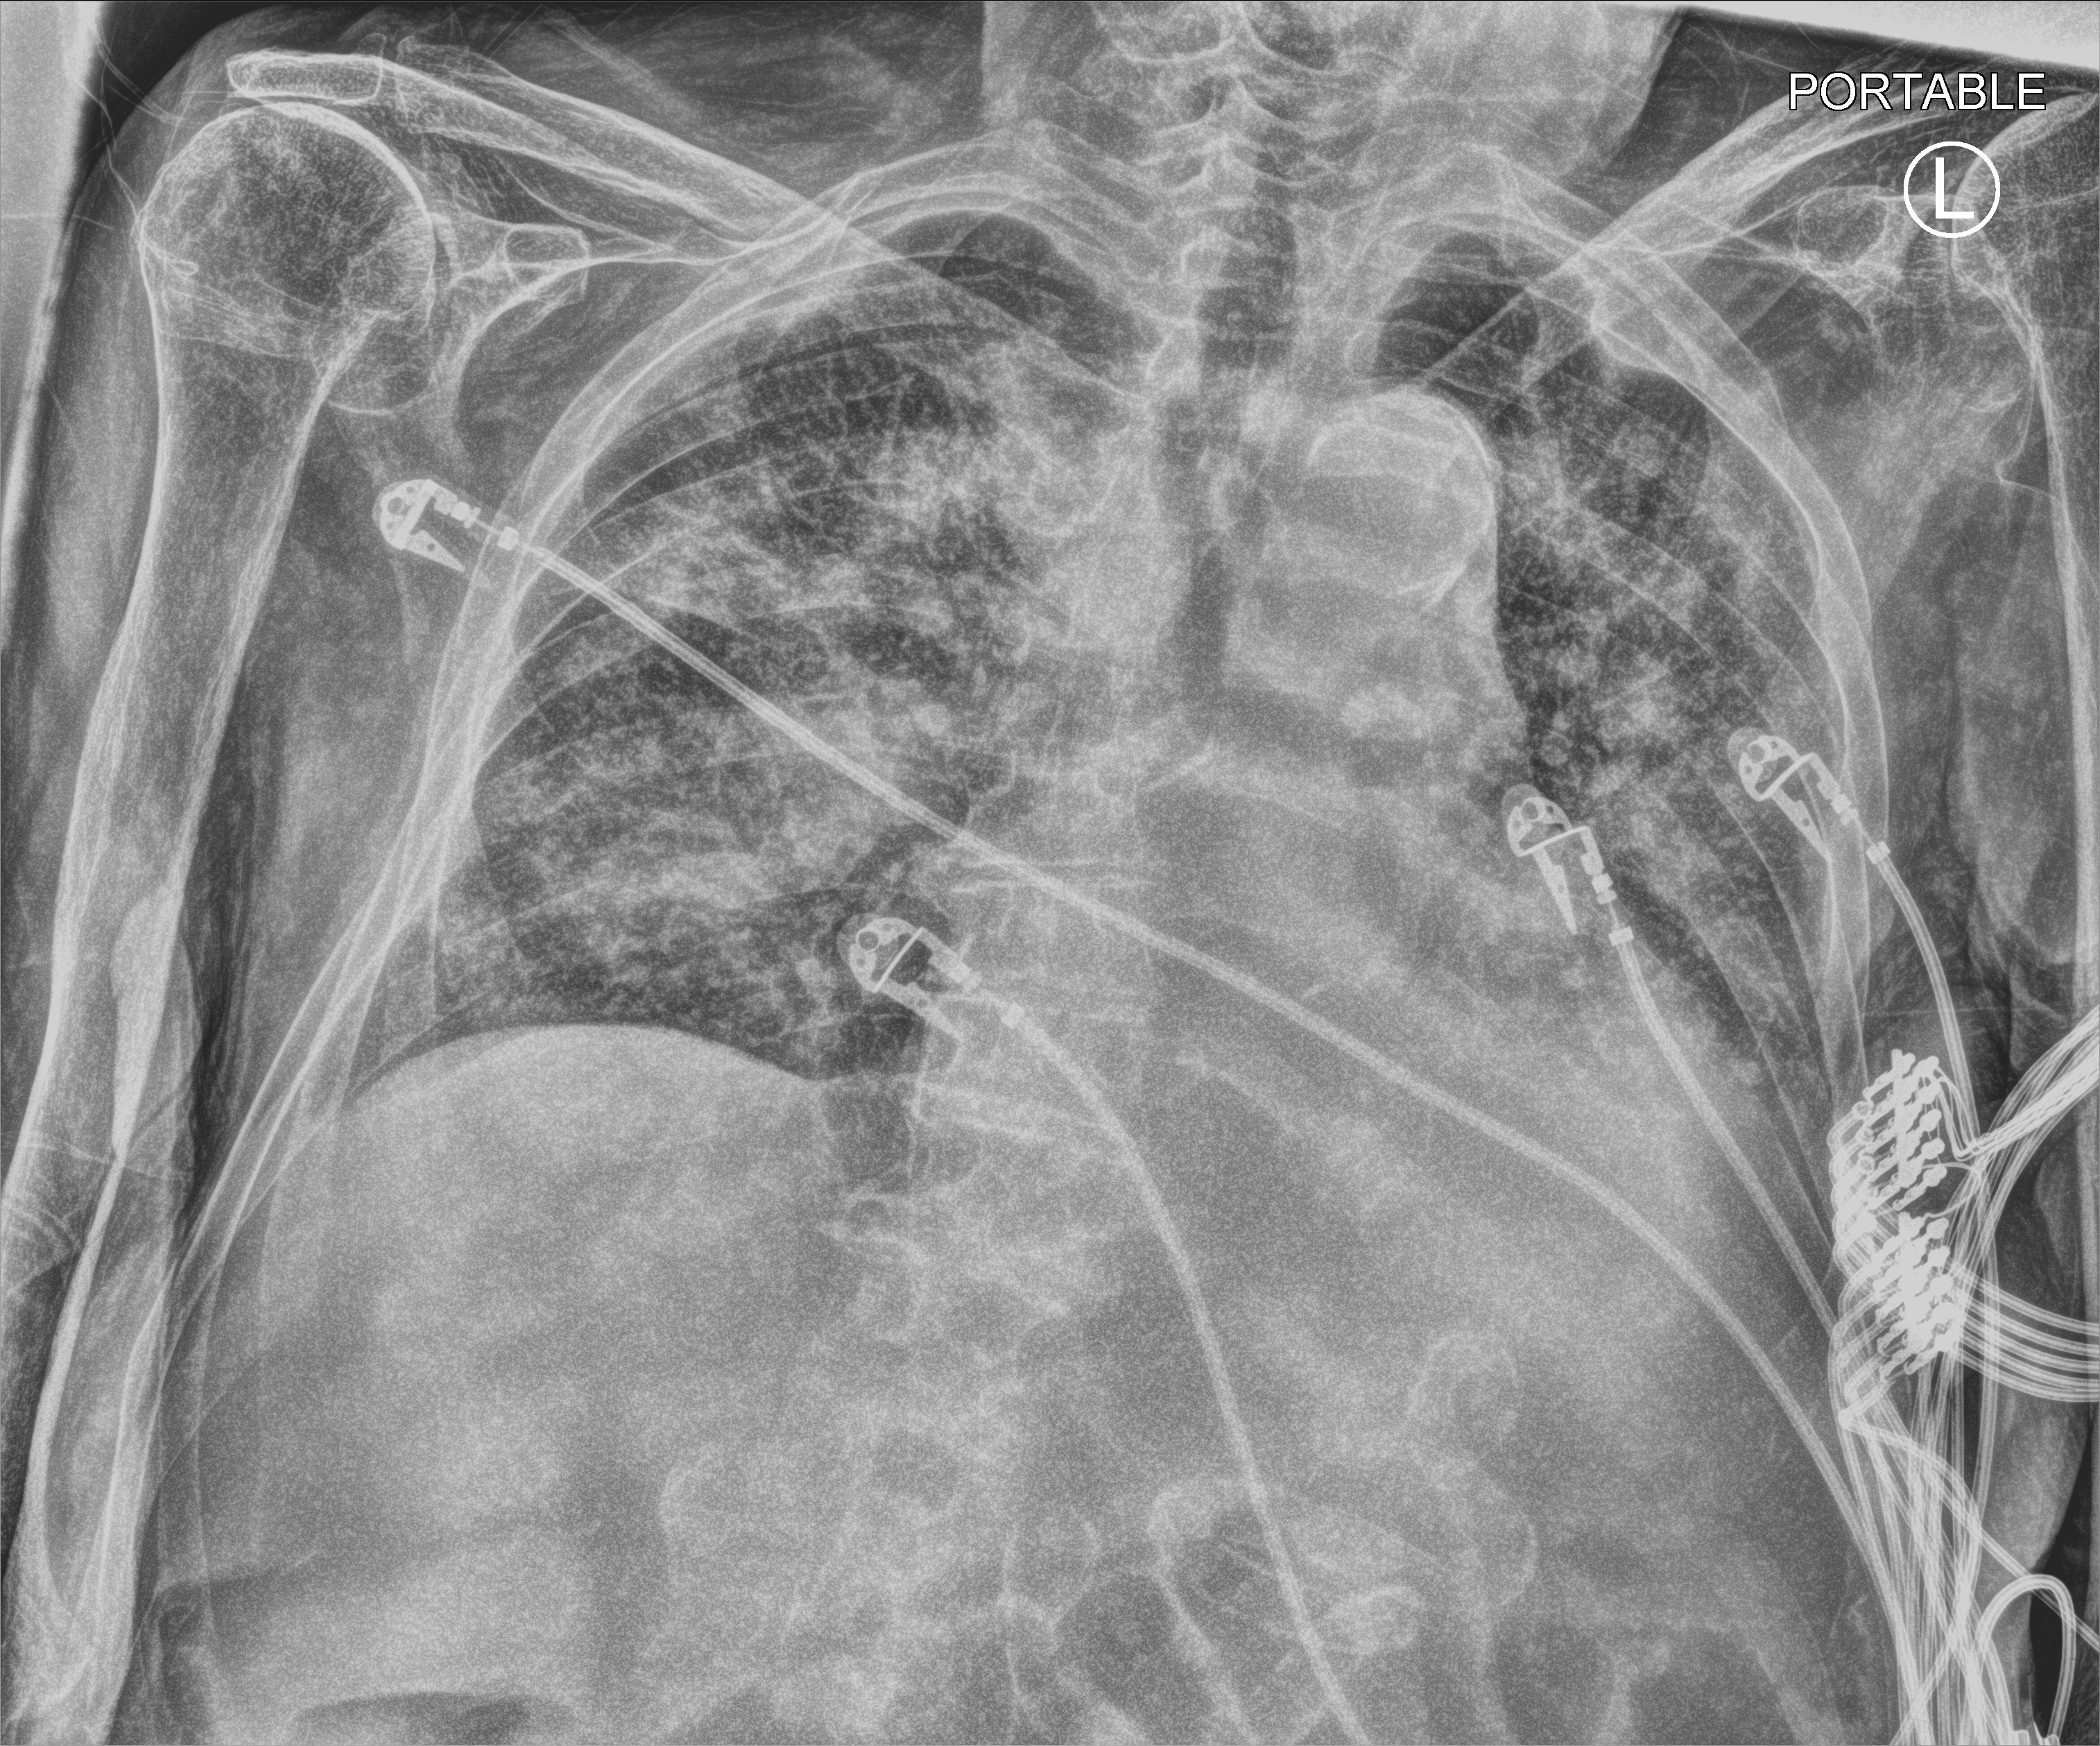
Bedside chest radiograph (computed radiography); anteroposterior (AP) projection. Patient hospitalised with COVID-19; male, aged 75–90 years.
Admission-level facts for this patient (not findings on this image; timing relative to this image not recorded):
- mechanically ventilated during this hospital stay: no